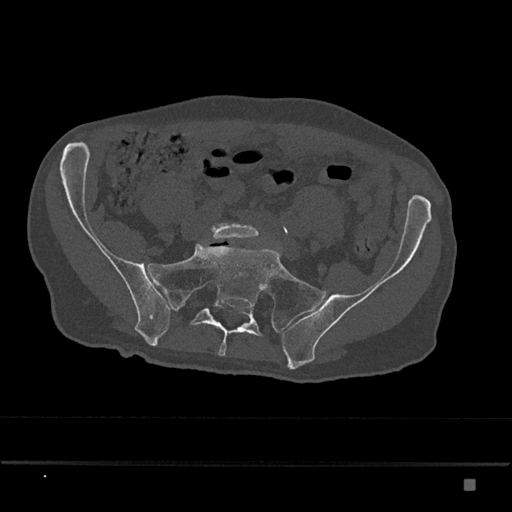
CT including the spine, one axial slice. Position 212 of 797 along the scan axis. Reconstruction kernel Br40s/3. 120 kVp. Bone window (W 1800 / L 400 HU). 512 × 512 image matrix, field of view 390 × 390 mm. Patient: male, 72 years. From the clinical record (not read from this slice): primary cancer: prostate.
Annotated regions visible in this slice (semi-automatically segmented with operator editing):
- L5 vertebra: box from (x=211, y=223) to (x=259, y=241) px